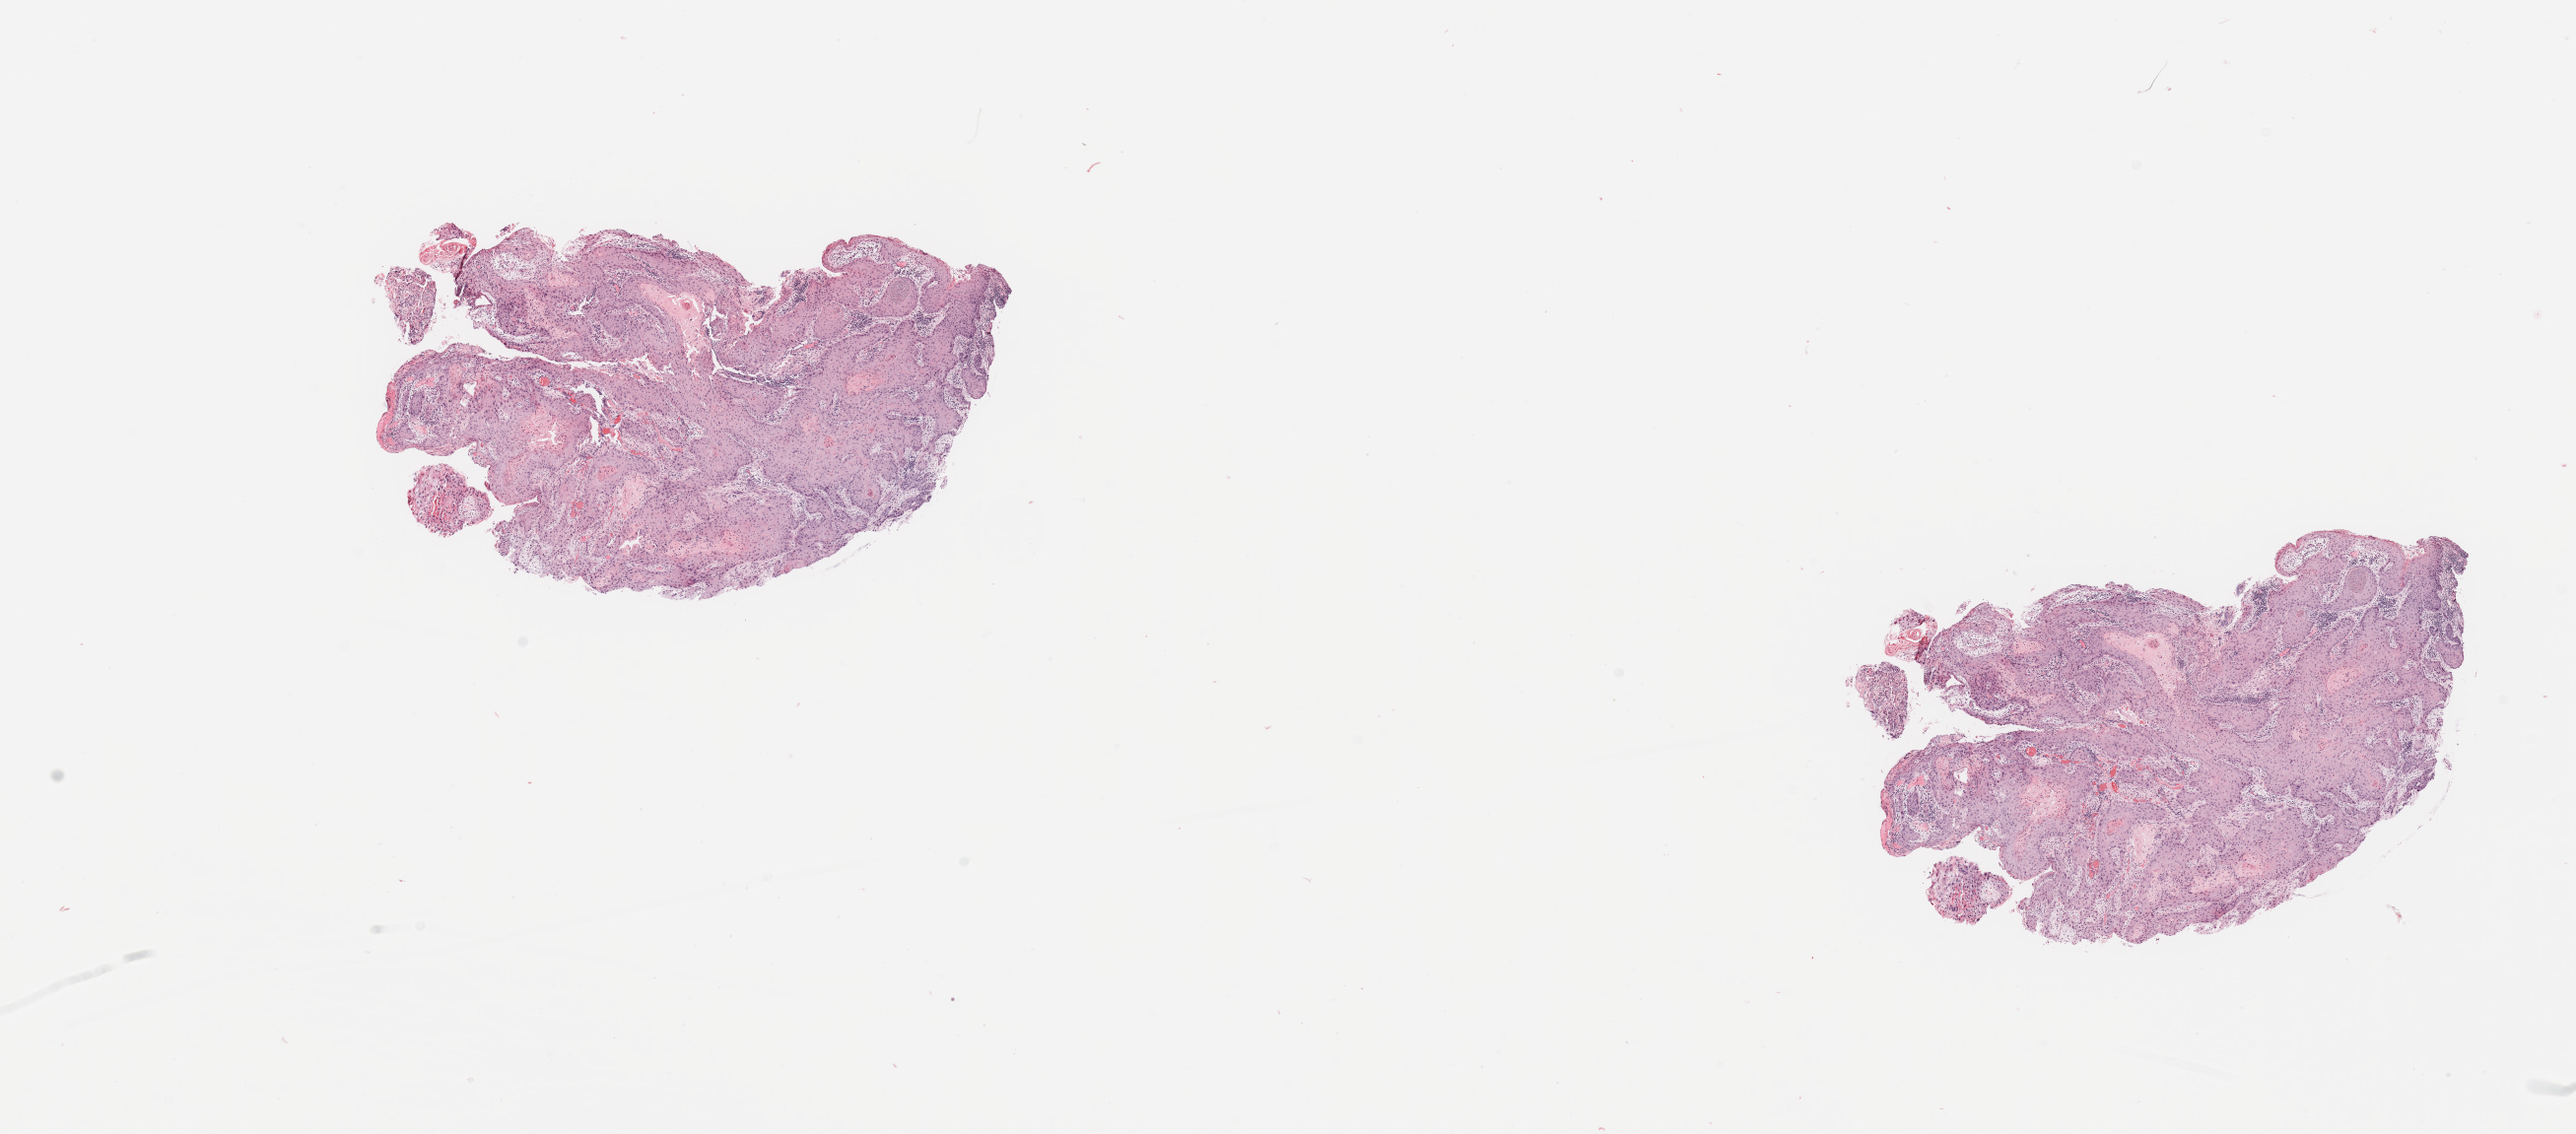
Whole-slide histology image, H&E-stained, shown as a low-resolution overview of the whole scanned area (about 20.7 x 9.1 mm, acquisition: 20x scan). Head and neck, tissue type not recorded. Patient: female, age 67 years.
* patient diagnosis: Squamous cell carcinoma, NOS (overlapping lesion of lip, oral cavity and pharynx)